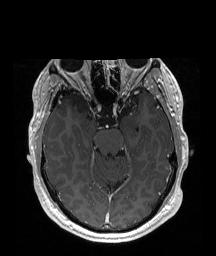
Brain MRI from a brain-tumour surgery series, one axial slice; position 124 of 192 along the scan axis; T1-weighted post-contrast; 1 mm slice thickness; 216 × 256 image matrix, field of view 219 × 260 mm. From the clinical record (not read from this slice): histopathology: Astrocytoma; WHO grade: 2; IDH mutation: yes.
Outlined on this slice (expert manual segmentation):
- tumour: bounding box <69,92,91,114> (left, top, right, bottom; pixels)